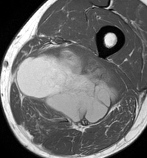
MRI of an extremity soft-tissue mass, one axial slice. Position 51 of 86 along the scan axis. MR volume resampled by the dataset authors to the PET/CT grid (not the native acquisition matrix). 147 × 158 image matrix. Male patient. From the clinical record (not read from this slice): histological type: undifferentiated pleomorphic liposarcoma; grade: high; site of the primary tumour: left thigh.
Outlined on this slice (expert contour drawn on MRI and transferred to this co-registered scan by the dataset authors):
- gross tumour volume including surrounding oedema: bounding box (x1, y1, x2, y2) in pixels: (16, 46, 120, 130)
- gross tumour volume (mass): (16, 46, 120, 128)